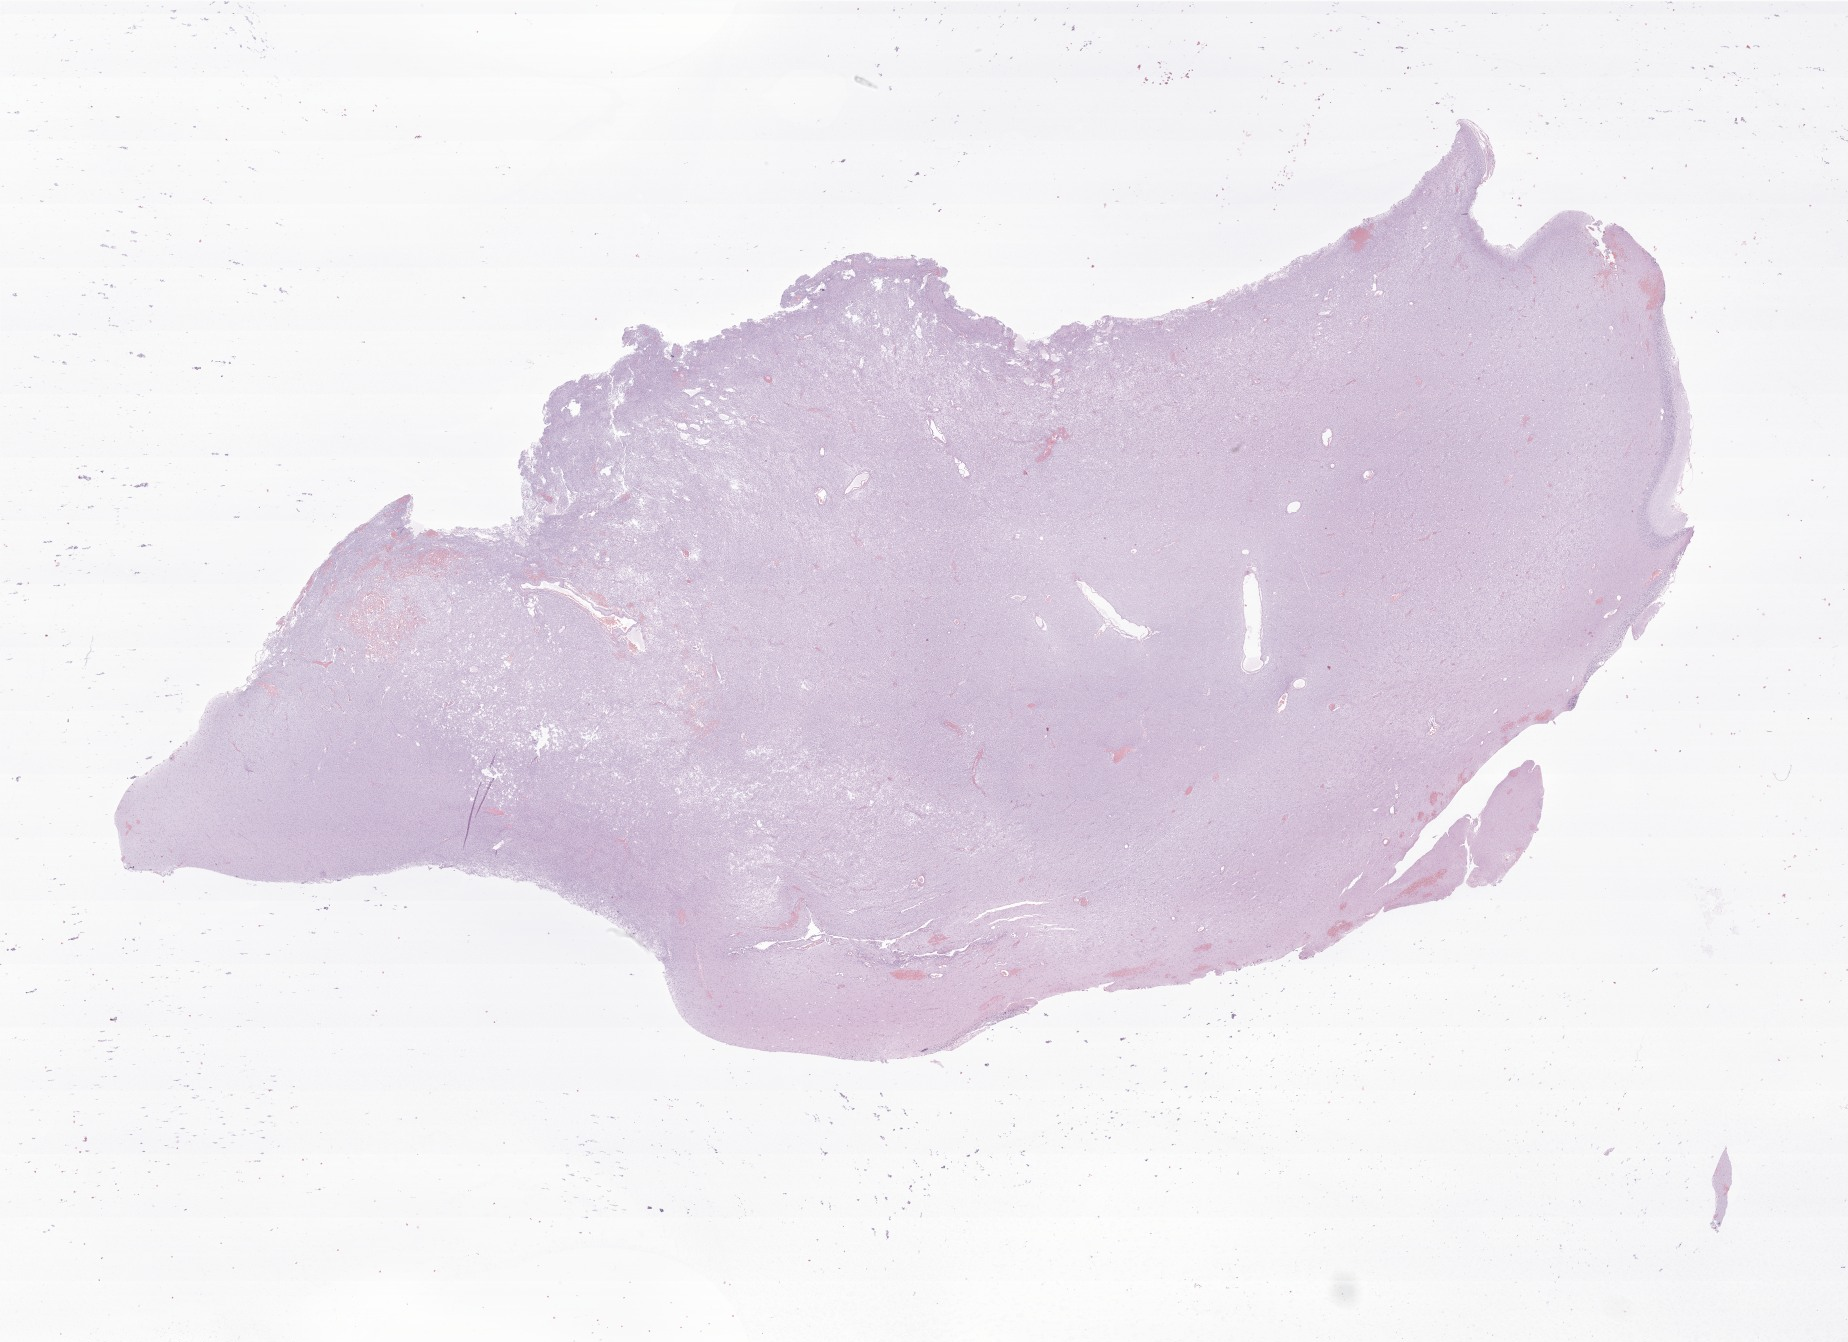
Haematoxylin and eosin whole-slide image of tumor tissue from the brain stem, a low-resolution overview of the entire scanned area, about 31.2 x 22.6 mm, FFPE section. Patient: female, age 34 months (2 years 10 months).
Diagnosis (ICD-O-3 morphology term): Glioma, malignant.